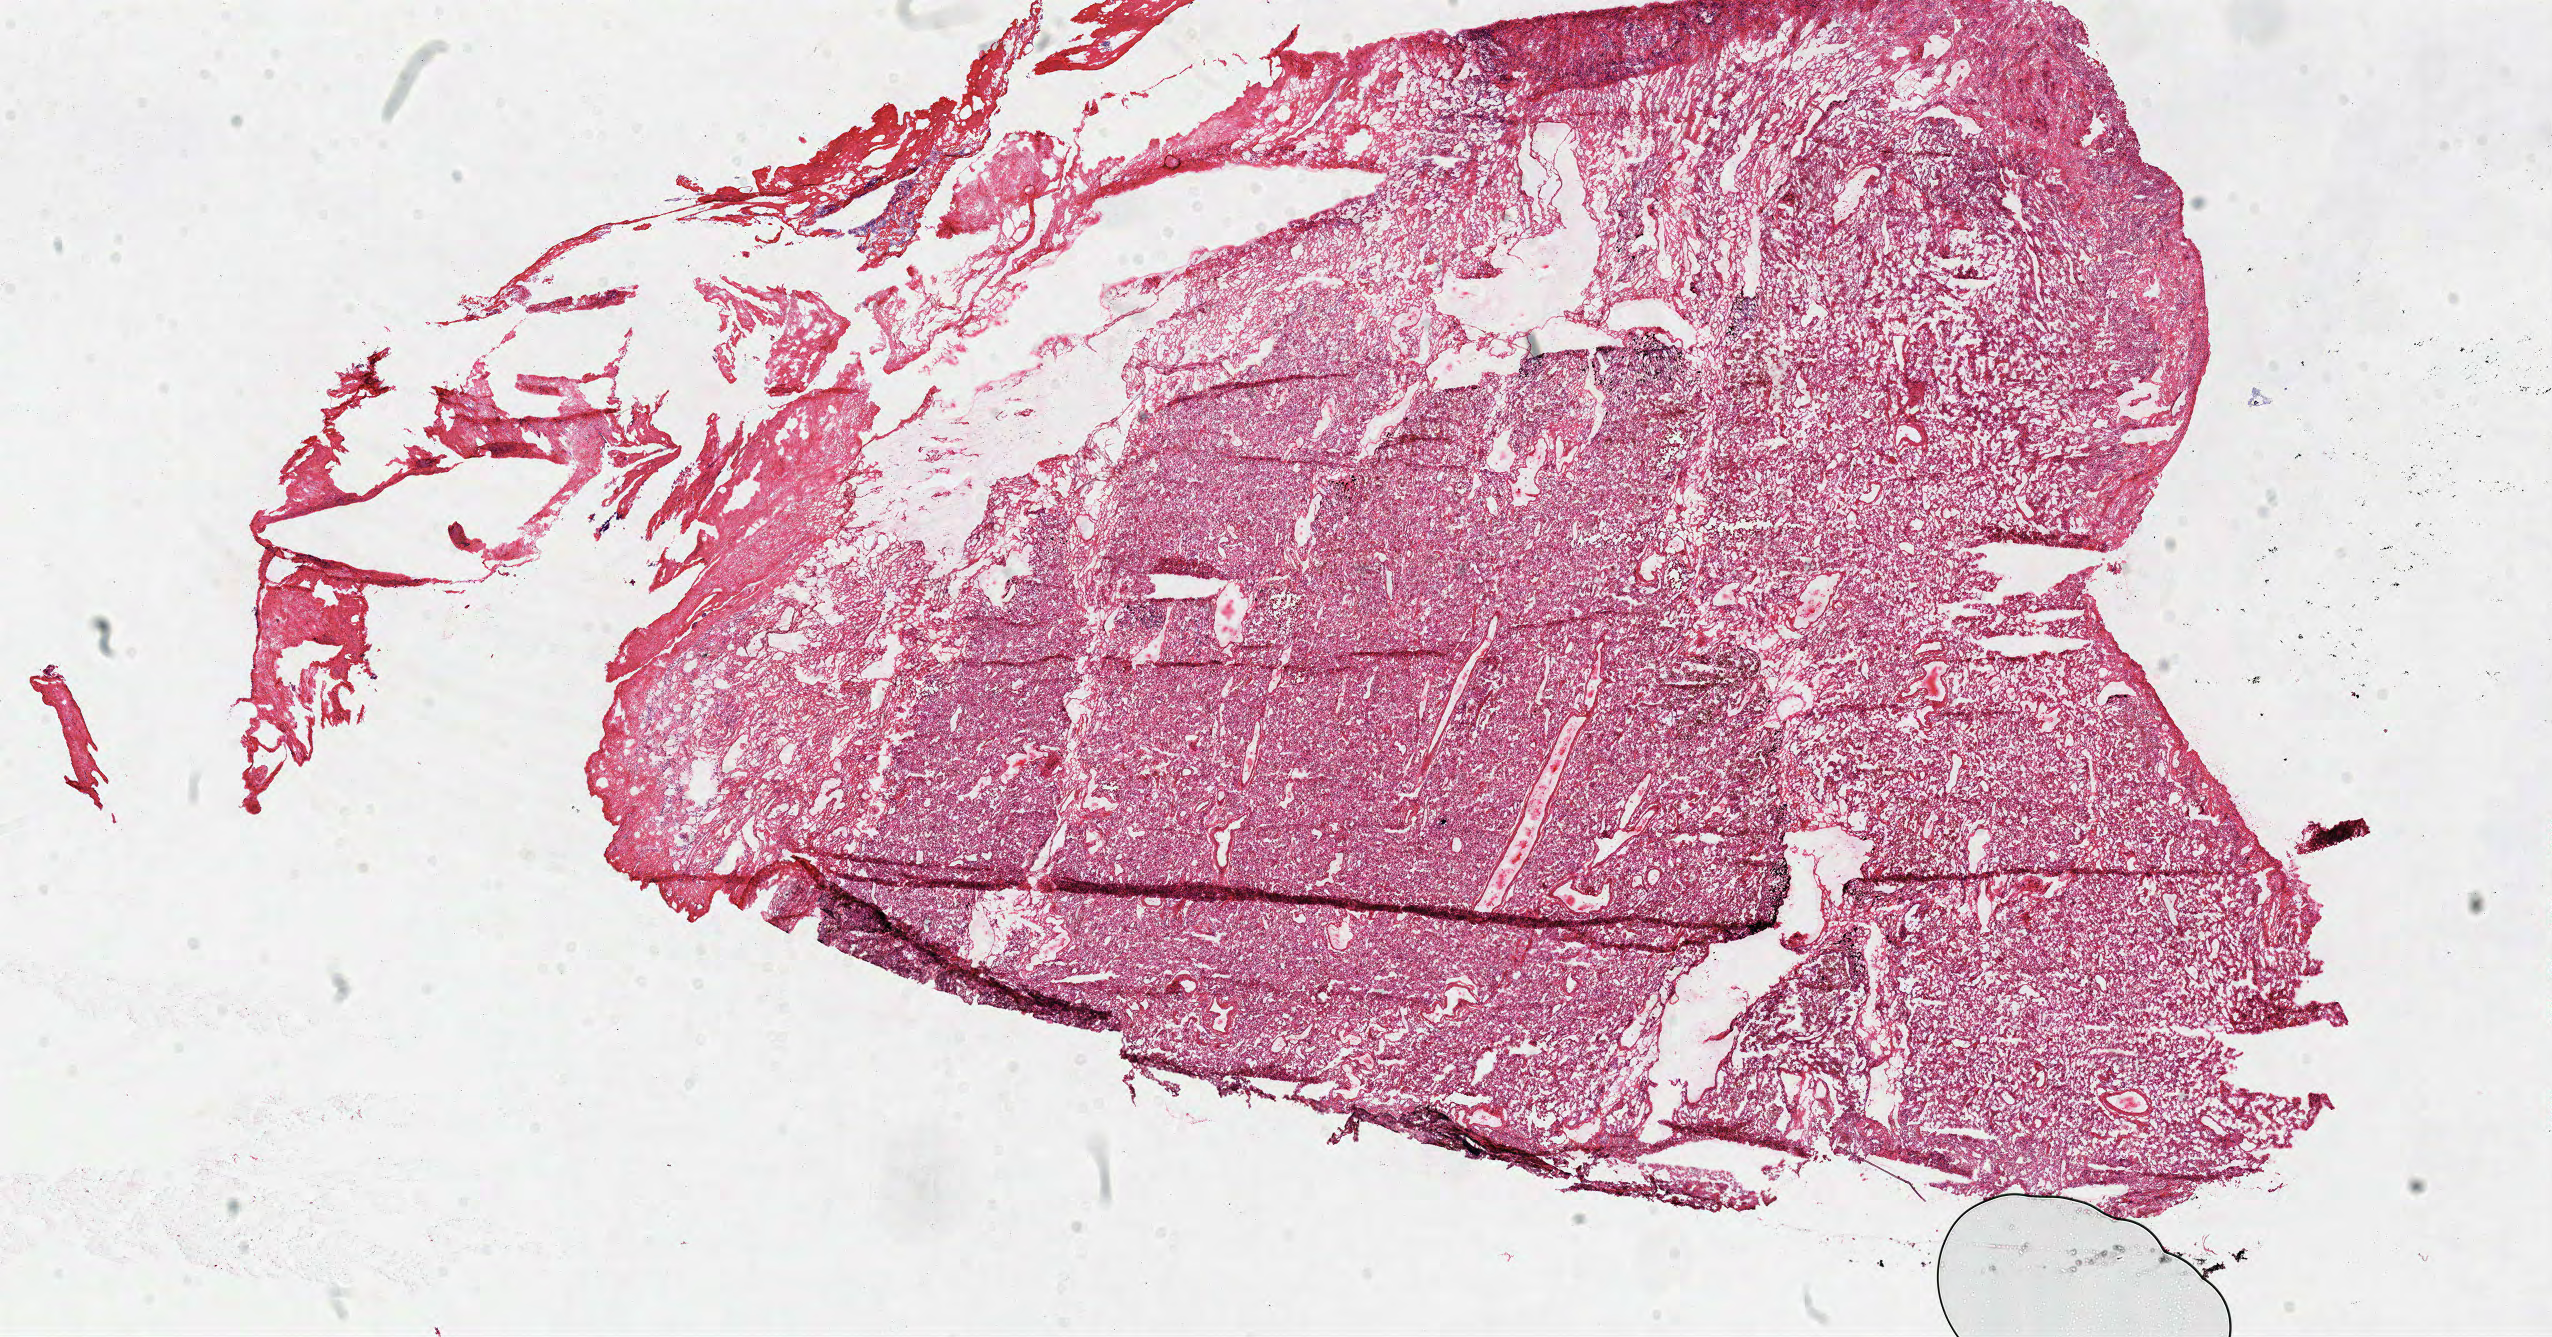
Digitized H&E tissue section (whole slide) — a low-resolution overview of the entire scanned area, about 20.1 x 10.5 mm (from a 40x scan). Frozen section from the top of the tissue portion. Solid tissue normal (non-tumour tissue) sample from the lung. Male patient; age at initial diagnosis 47 years.
• this section: solid tissue normal (non-tumour) sample from the same patient
• patient diagnosis: Adenocarcinoma with mixed subtypes (lower lobe, lung)